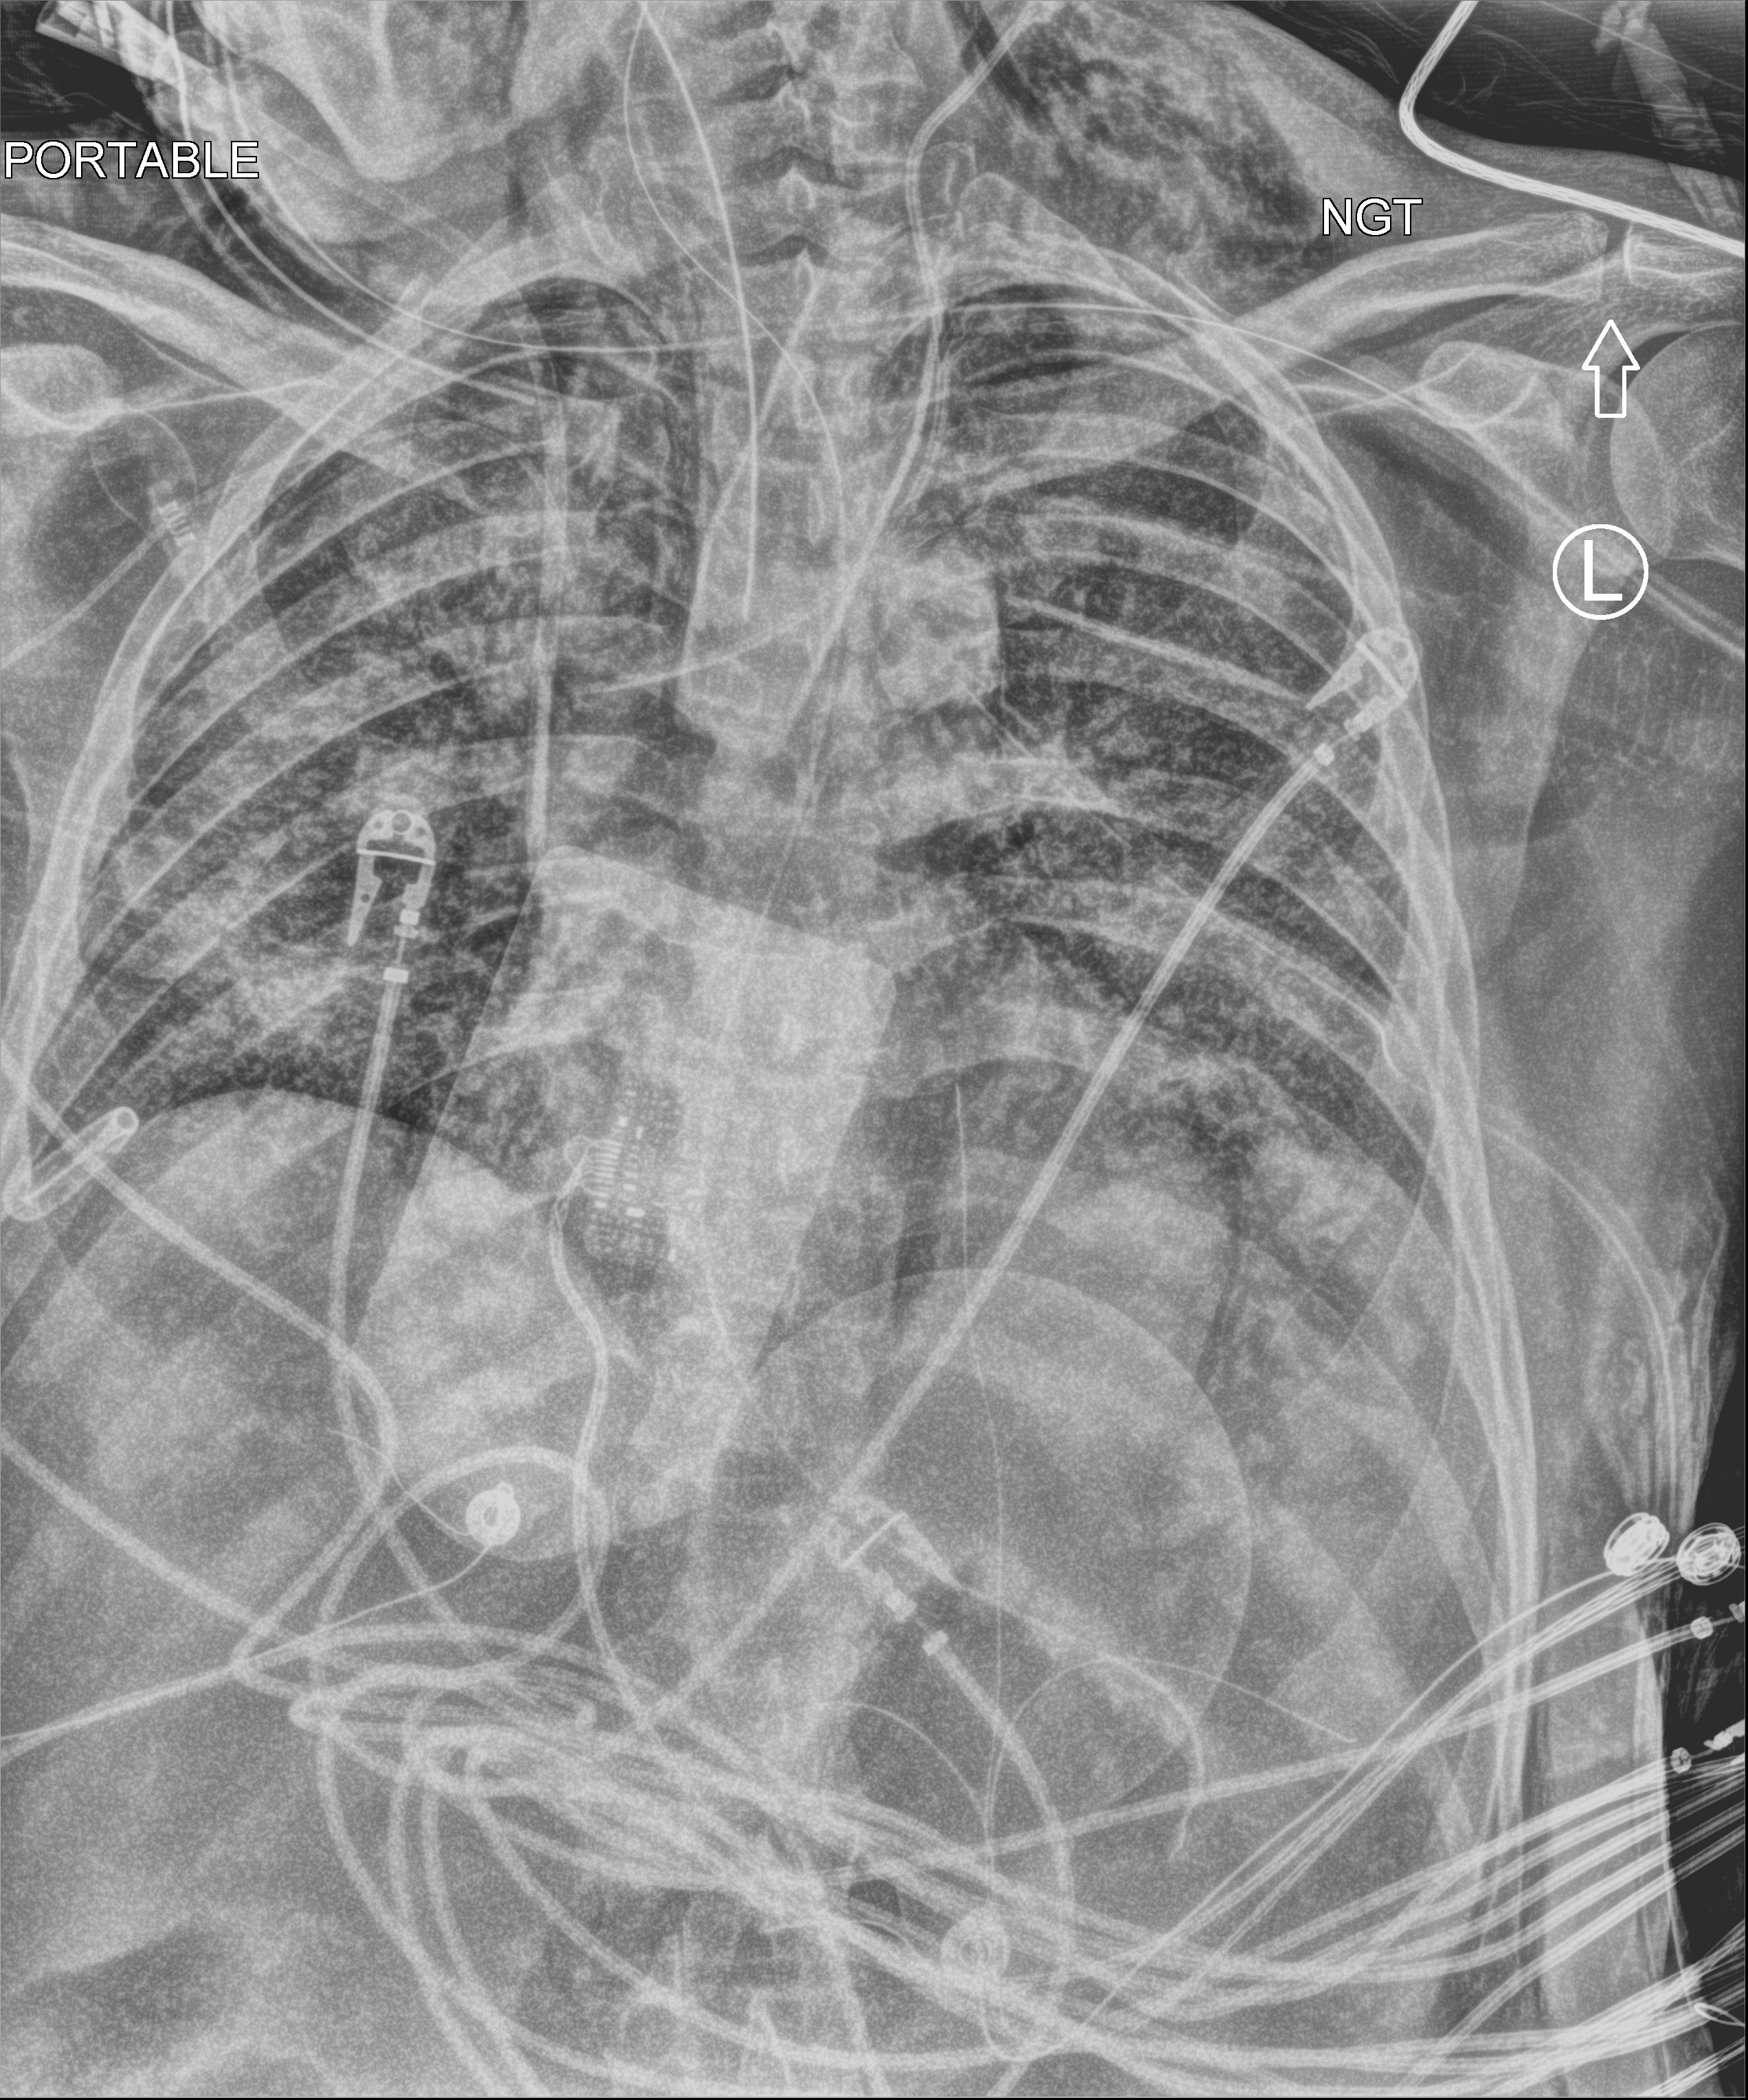
Portable chest radiograph. Patient hospitalised with COVID-19; male, aged 18–59 years.
Admission-level facts for this patient (not findings on this image; timing relative to this image not recorded):
- diabetes (admission record): no
- admitted to intensive care during this hospital stay: yes
- COPD (admission record): no